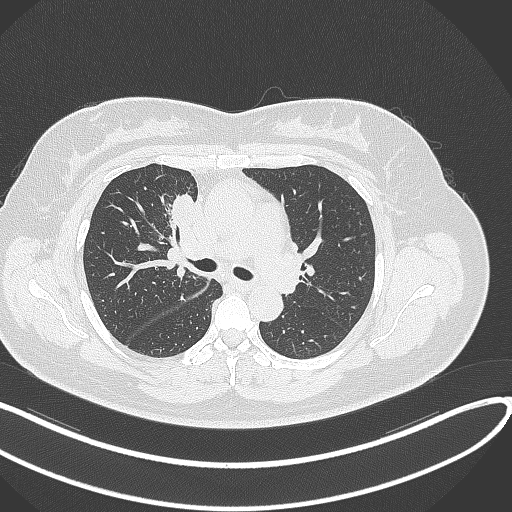
Chest CT, one axial slice. Position 174 of 303 along the scan axis. Reconstruction kernel B70f. 120 kVp. Lung window (W 1500 / L -600 HU). 1 mm slice thickness. 512 × 512 image matrix. Patient: female, 46 years. Case-level facts recorded for this patient, not image findings: clinical TNM (as recorded): T2a N1 M0.
Annotated regions visible in this slice (bounding box drawn by a radiologist):
- lung tumour (recorded histology: adenocarcinoma): box from (x=170, y=190) to (x=199, y=232) px